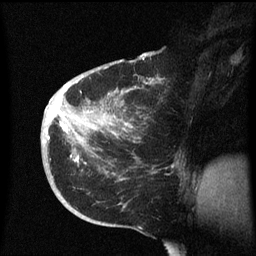
Breast MRI (dynamic contrast-enhanced), one sagittal slice; slice 29 of 60 in the series (ordered by position); dynamic contrast-enhanced series, image 2 of 3 at this slice position (ordered by acquisition); 1.5 T; TE 4.2 ms, TR 8.4 ms; 2.3 mm slice thickness; 256 × 256 image matrix, field of view 200 × 200 mm. Female patient, age 38 years. Case-level facts recorded for this patient, not image findings: setting: breast cancer imaged before/during neoadjuvant chemotherapy; receptor status: HER2-positive.
Outlined on this slice (semi-automatically segmented with operator editing):
- analysis volume of interest (the breast-tissue region the enhancement analysis was run in; not a lesion): bounding box (x1, y1, x2, y2) in pixels: (41, 78, 188, 213)
- tumour enhancement mask (voxels above the 70 % enhancement threshold inside the analysis volume of interest): (48, 86, 135, 163)